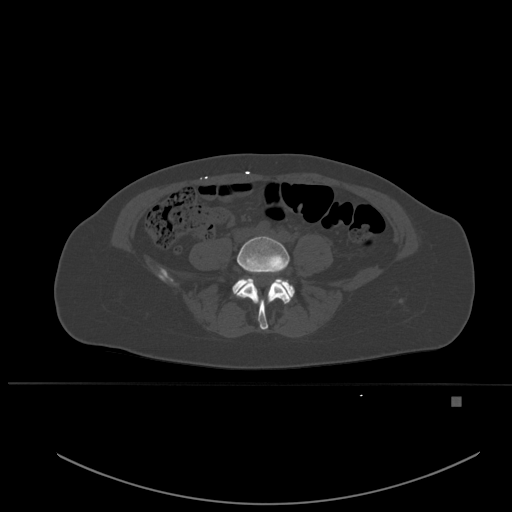
CT including the spine, one axial slice; slice 166 of 651 in the series (ordered by position); bone window (W 1800 / L 400 HU); 1.5 mm slice thickness; 512 × 512 image matrix. Patient: female, 49 years. From the clinical record (not read from this slice): primary cancer: breast; vertebrae with lytic lesions (as recorded): L3, T12, L4.
Annotated regions visible in this slice (semi-automatic segmentation, software-assisted and operator-edited):
- L4 vertebra: bounding box <237,236,291,330> (left, top, right, bottom; pixels)
- L5 vertebra: <232,278,295,300>